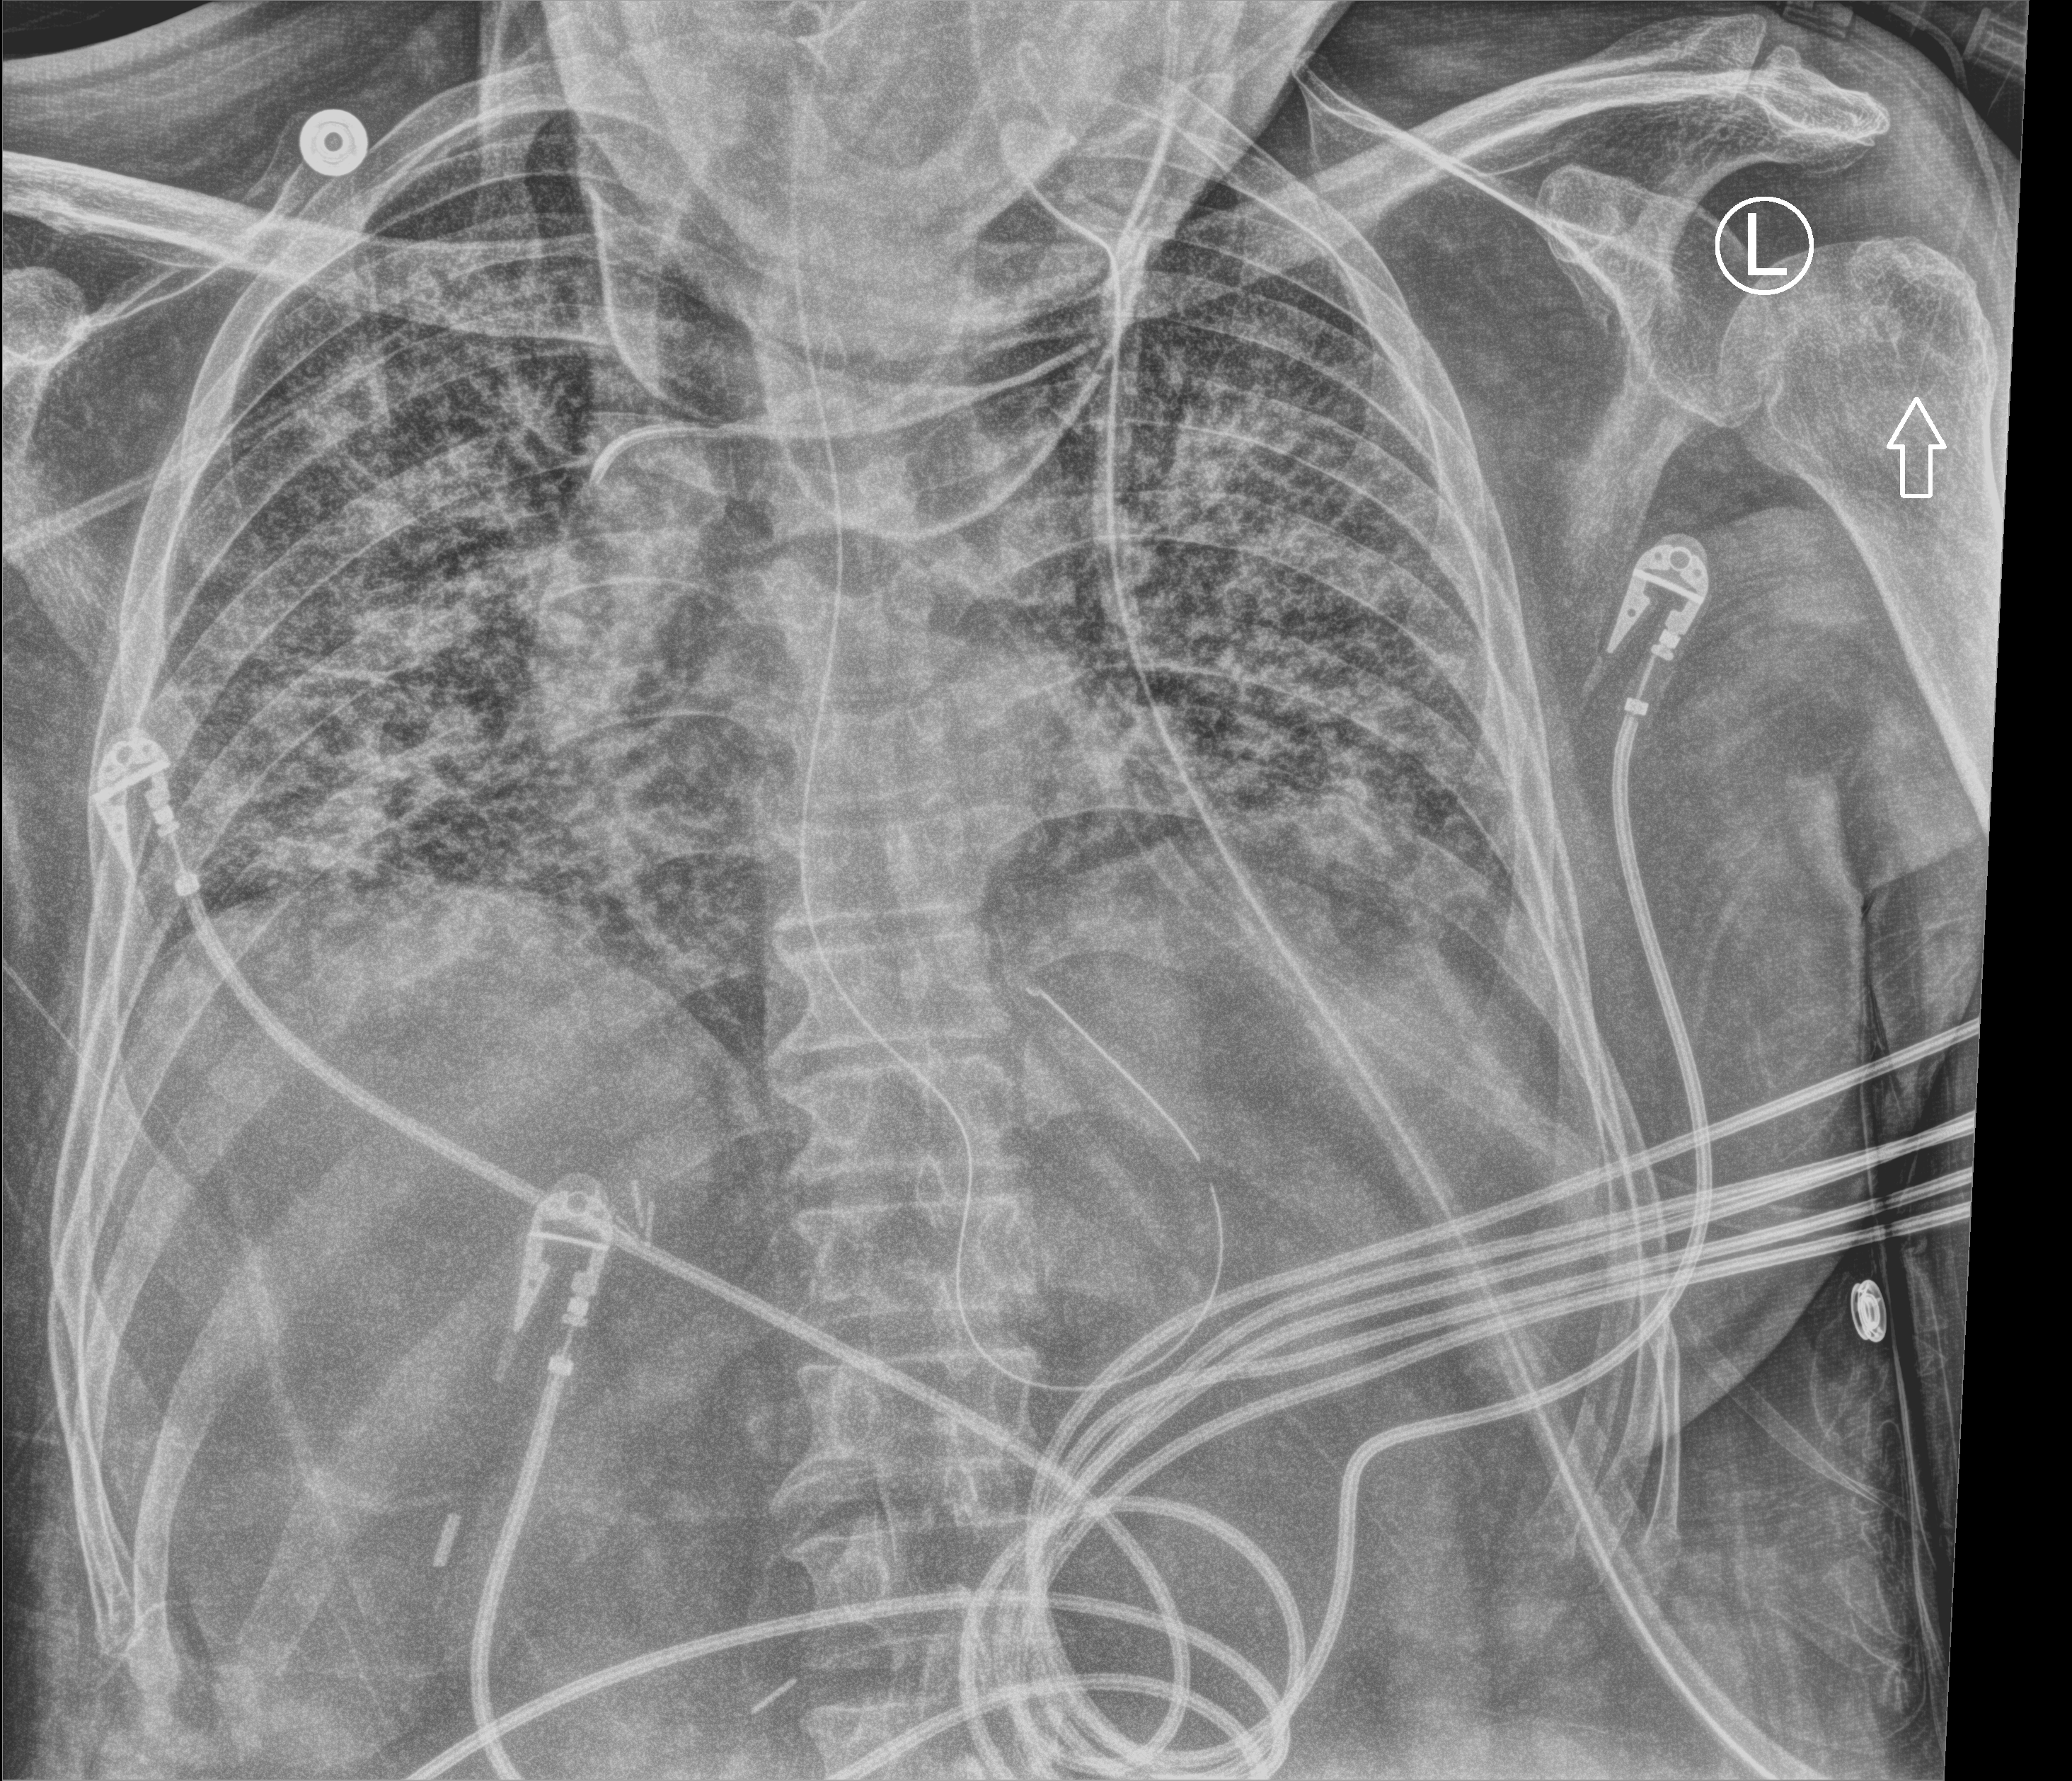
Bedside chest radiograph (computed radiography), anteroposterior (AP) projection. Male patient hospitalised with COVID-19, age 60–74 years.
Hospital-stay facts (about this admission, not read from this image; timing relative to this image not recorded):
- mechanically ventilated during this hospital stay: yes
- admitted to intensive care during this hospital stay: yes
- COPD (admission record): no